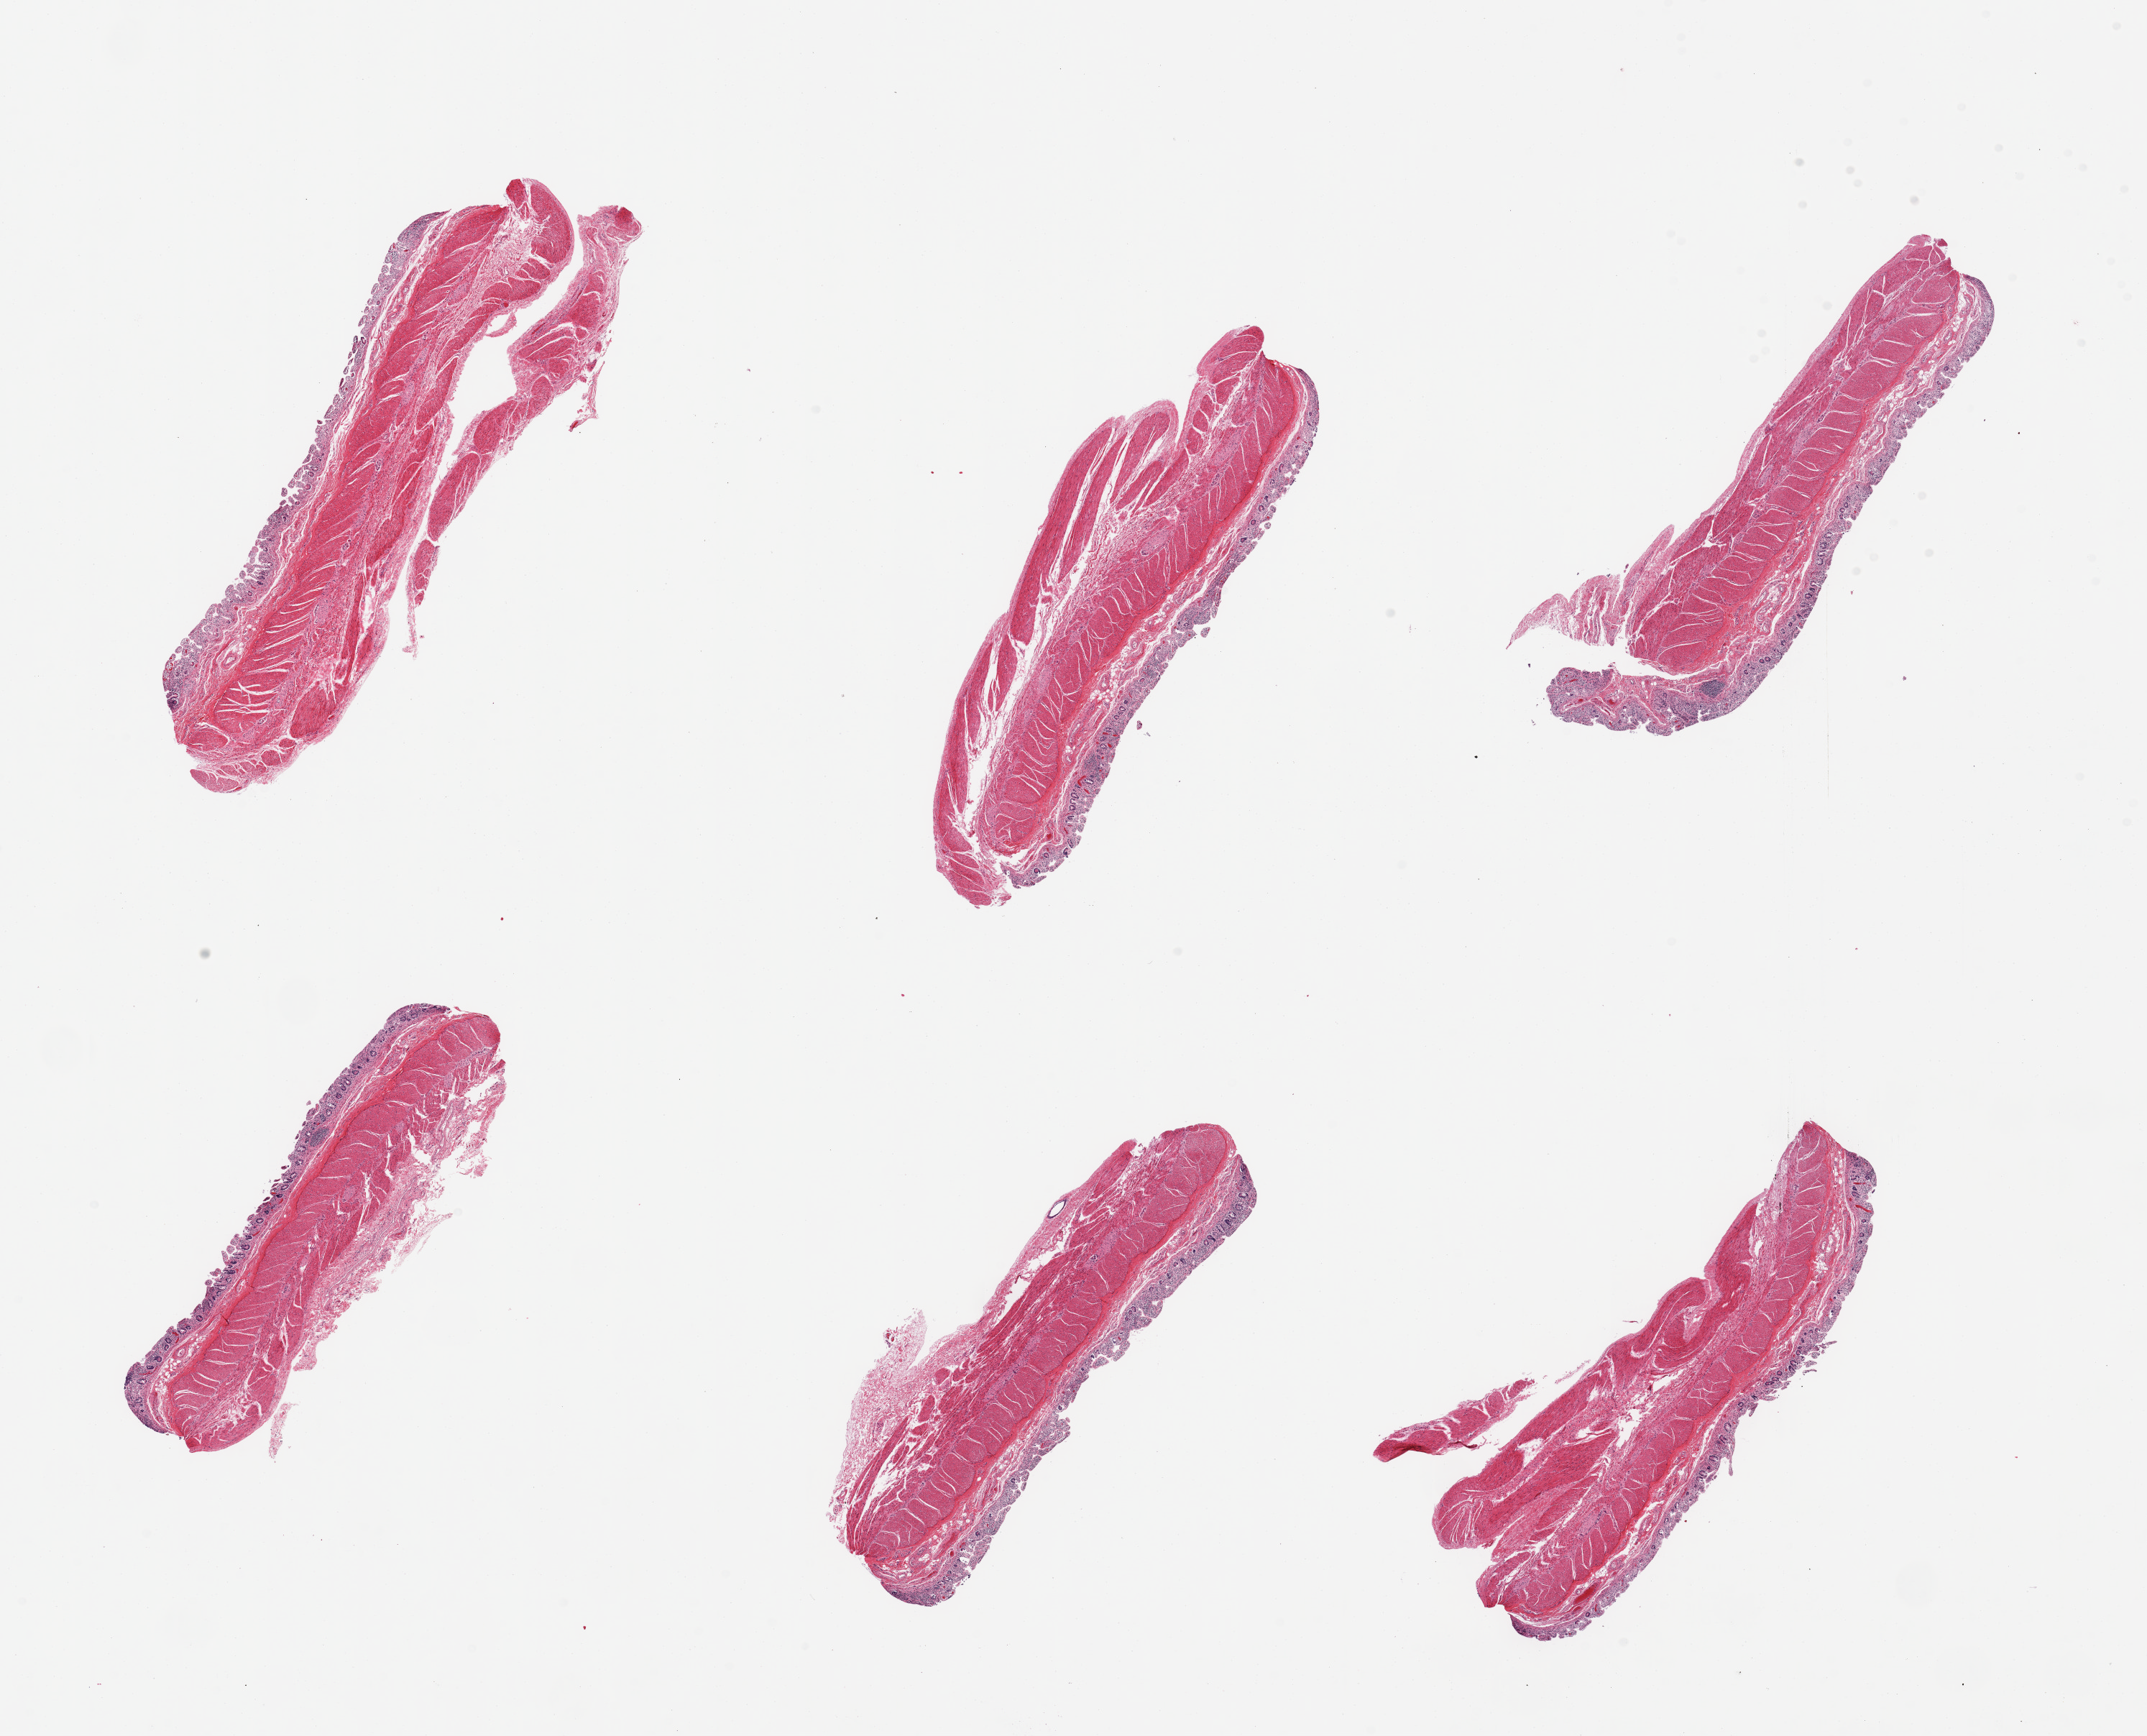
Hematoxylin and eosin (H&E) whole-slide image — shown as a low-resolution overview of the whole scanned area (about 23.6 x 19.1 mm). PAXgene-fixed paraffin-embedded (PFPE) section. Sampled site (target tissue): ileum. Tissue donor sample.
Reviewer comment on this tissue sample: 6 pieces; colon (full thickness) not ileum.